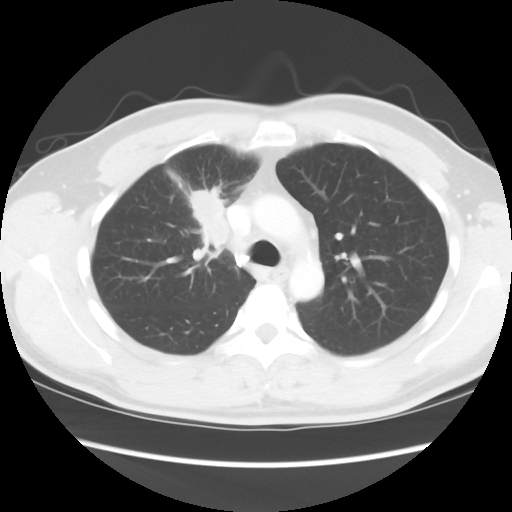
Chest CT, one axial slice. Slice 63 of 80 in the series (ordered by position). Reconstruction kernel STANDARD. 120 kVp. Lung window (W 1500 / L -600 HU). 5 mm slice thickness. 512 × 512 image matrix. Patient: male, 35 years. From the clinical record (not read from this slice): clinical TNM (as recorded): T1c N1 M1b.
Annotated regions visible in this slice (bounding box drawn by a radiologist):
- lung tumour (recorded histology: adenocarcinoma): bounding box [x1, y1, x2, y2] px = [186, 184, 232, 252]